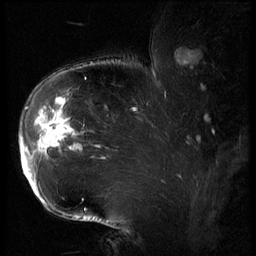
Breast MRI (dynamic contrast-enhanced), one sagittal slice; slice 45 of 62 in the series (ordered by position); 3 images stored at this slice position (order not interpretable as contrast timing); 1.5 T; TE 4.2 ms, TR 9 ms; 2.5 mm slice thickness; 256 × 256 image matrix, field of view 180 × 180 mm. Female patient, age 43 years. From the clinical record (not read from this slice): setting: breast cancer imaged before/during neoadjuvant chemotherapy; receptor status: HER2-positive.
Outlined on this slice (semi-automatic segmentation, software-assisted and operator-edited):
- analysis volume of interest (the breast-tissue region the enhancement analysis was run in; not a lesion): bounding box <20,90,82,203> (left, top, right, bottom; pixels)
- tumour enhancement mask (voxels above the 140 % enhancement threshold inside the analysis volume of interest): <20,98,78,195>